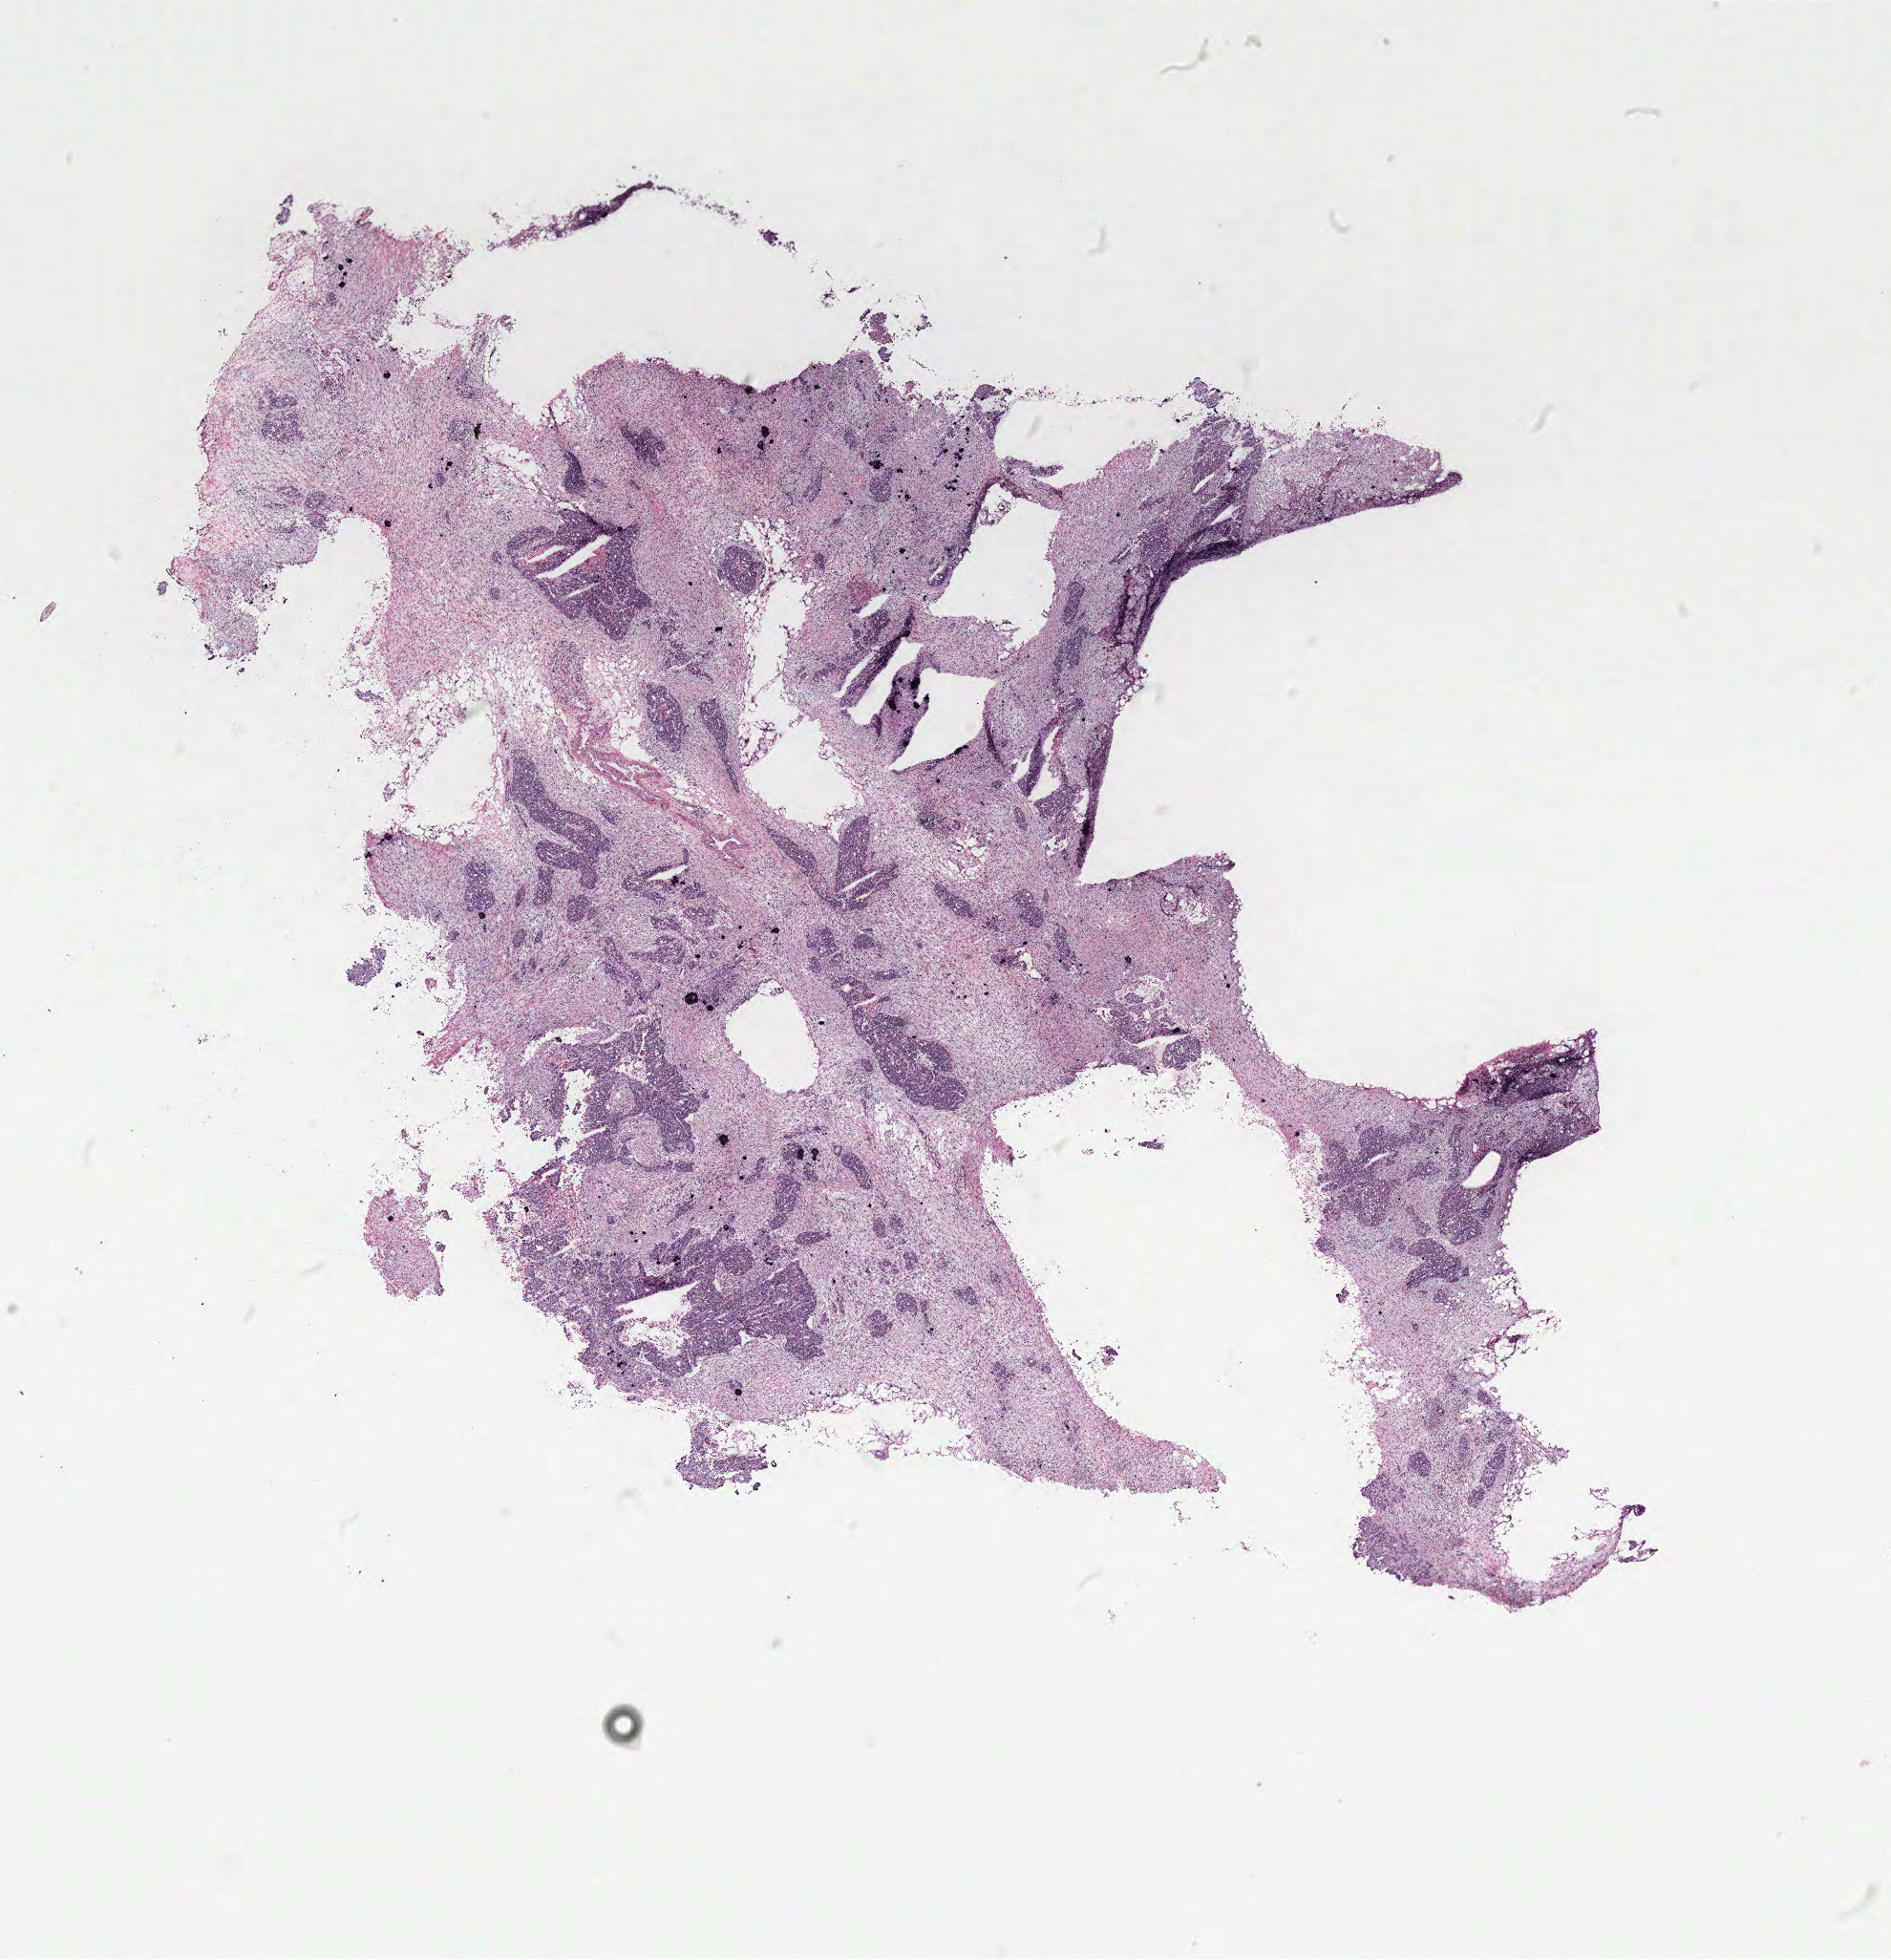
H&E-stained whole-slide image — shown as a low-resolution overview of the whole scanned area (about 15.8 x 16.4 mm, acquisition: 40x scan); tumour tissue sample, ovary. Female, 53 y/o.
* histologic diagnosis: Serous adenocarcinoma, NOS (fallopian tube)
* primary tumour site (as recorded): fallopian tube